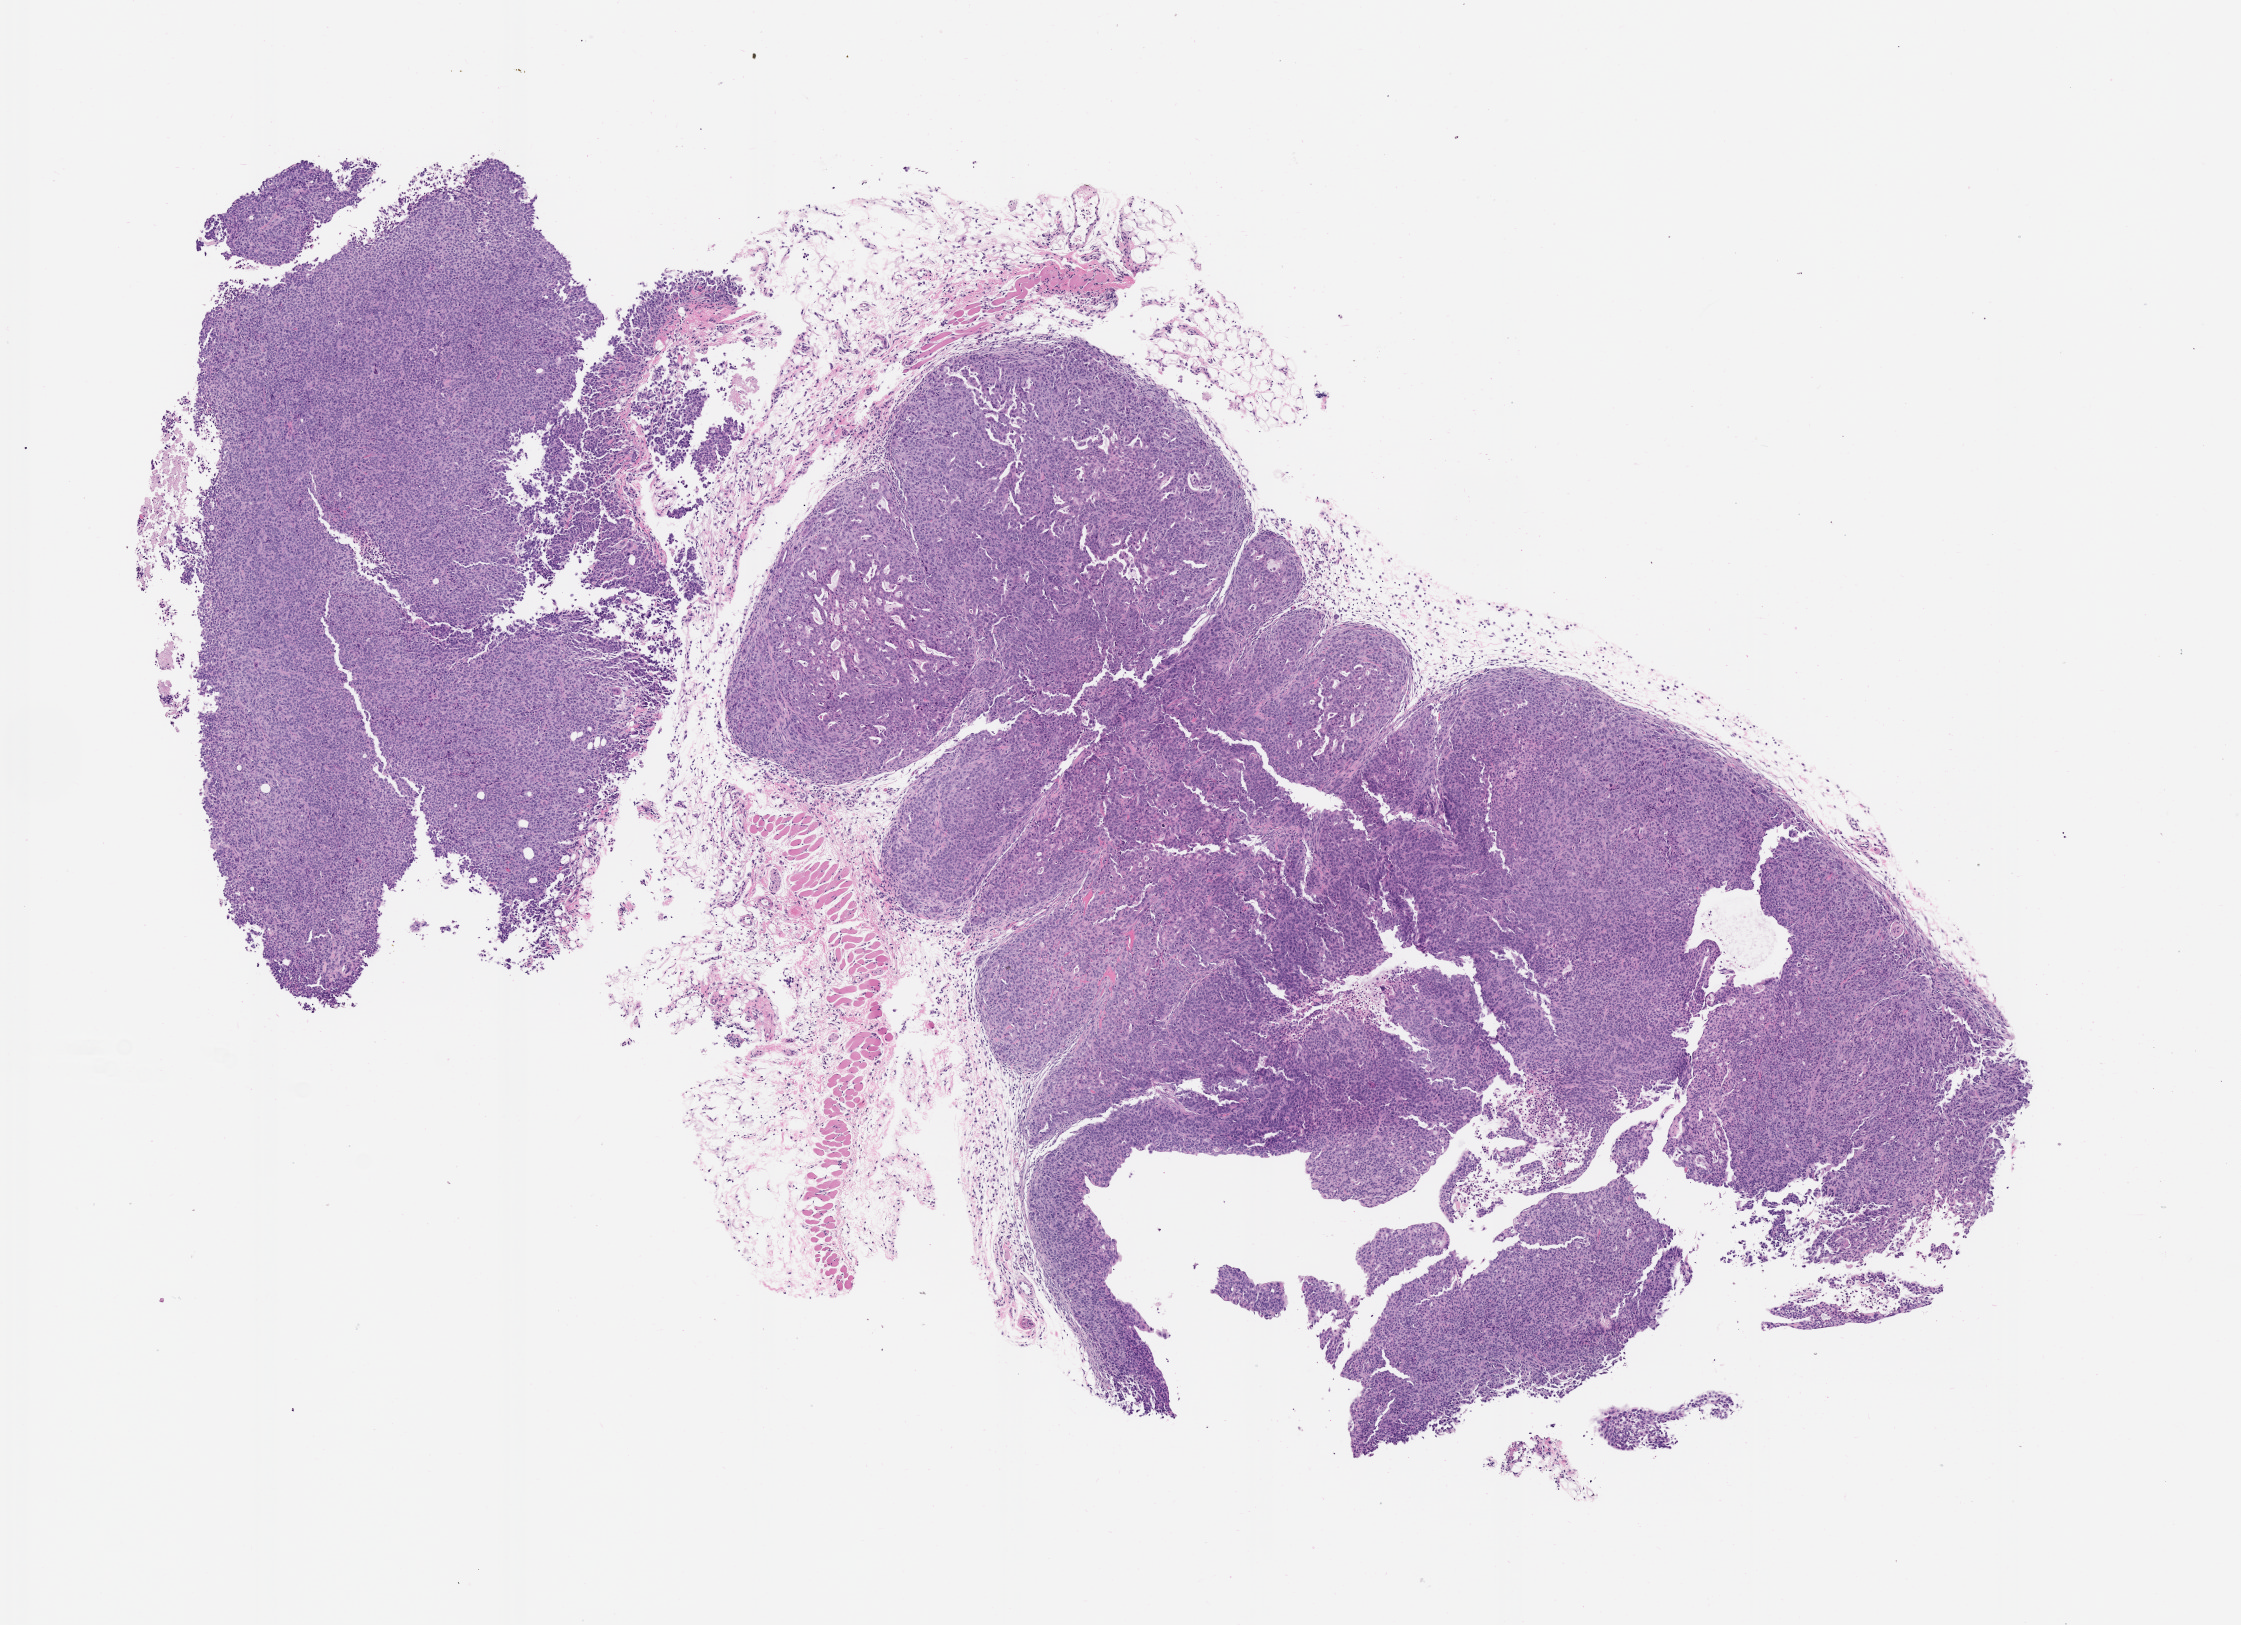
Haematoxylin and eosin whole-slide image of a patient-derived xenograft (PDX) tumor grown in a mouse, passage 1, shown as a low-resolution overview of the whole scanned area (about 9.0 x 6.5 mm). Formalin-fixed paraffin-embedded section. Tumor site category: pancreas.
Originating patient diagnosis: Pancreatic Adenocarcinoma.